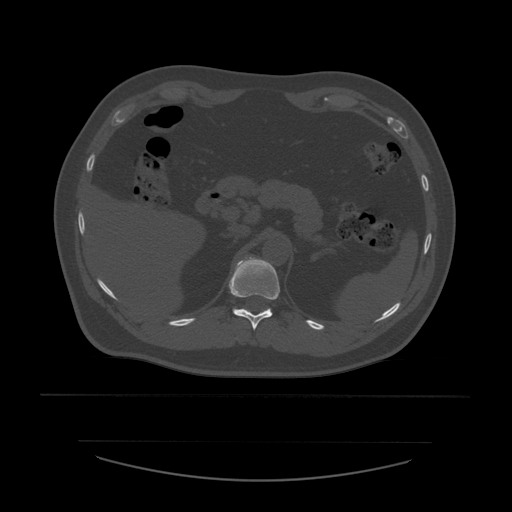
CT including the spine, one axial slice. Slice 271 of 532 in the series (ordered by position). Reconstruction kernel STANDARD. 120 kVp. Bone window (W 1800 / L 400 HU). 1.25 mm slice thickness. 512 × 512 image matrix, field of view 441 × 441 mm. Patient age 44 years. From the clinical record (not read from this slice): primary cancer: soft tissue sarcoma.
Structures marked on this image (semi-automatically segmented with operator editing):
- T11 vertebra: box from (x=229, y=257) to (x=280, y=331) px